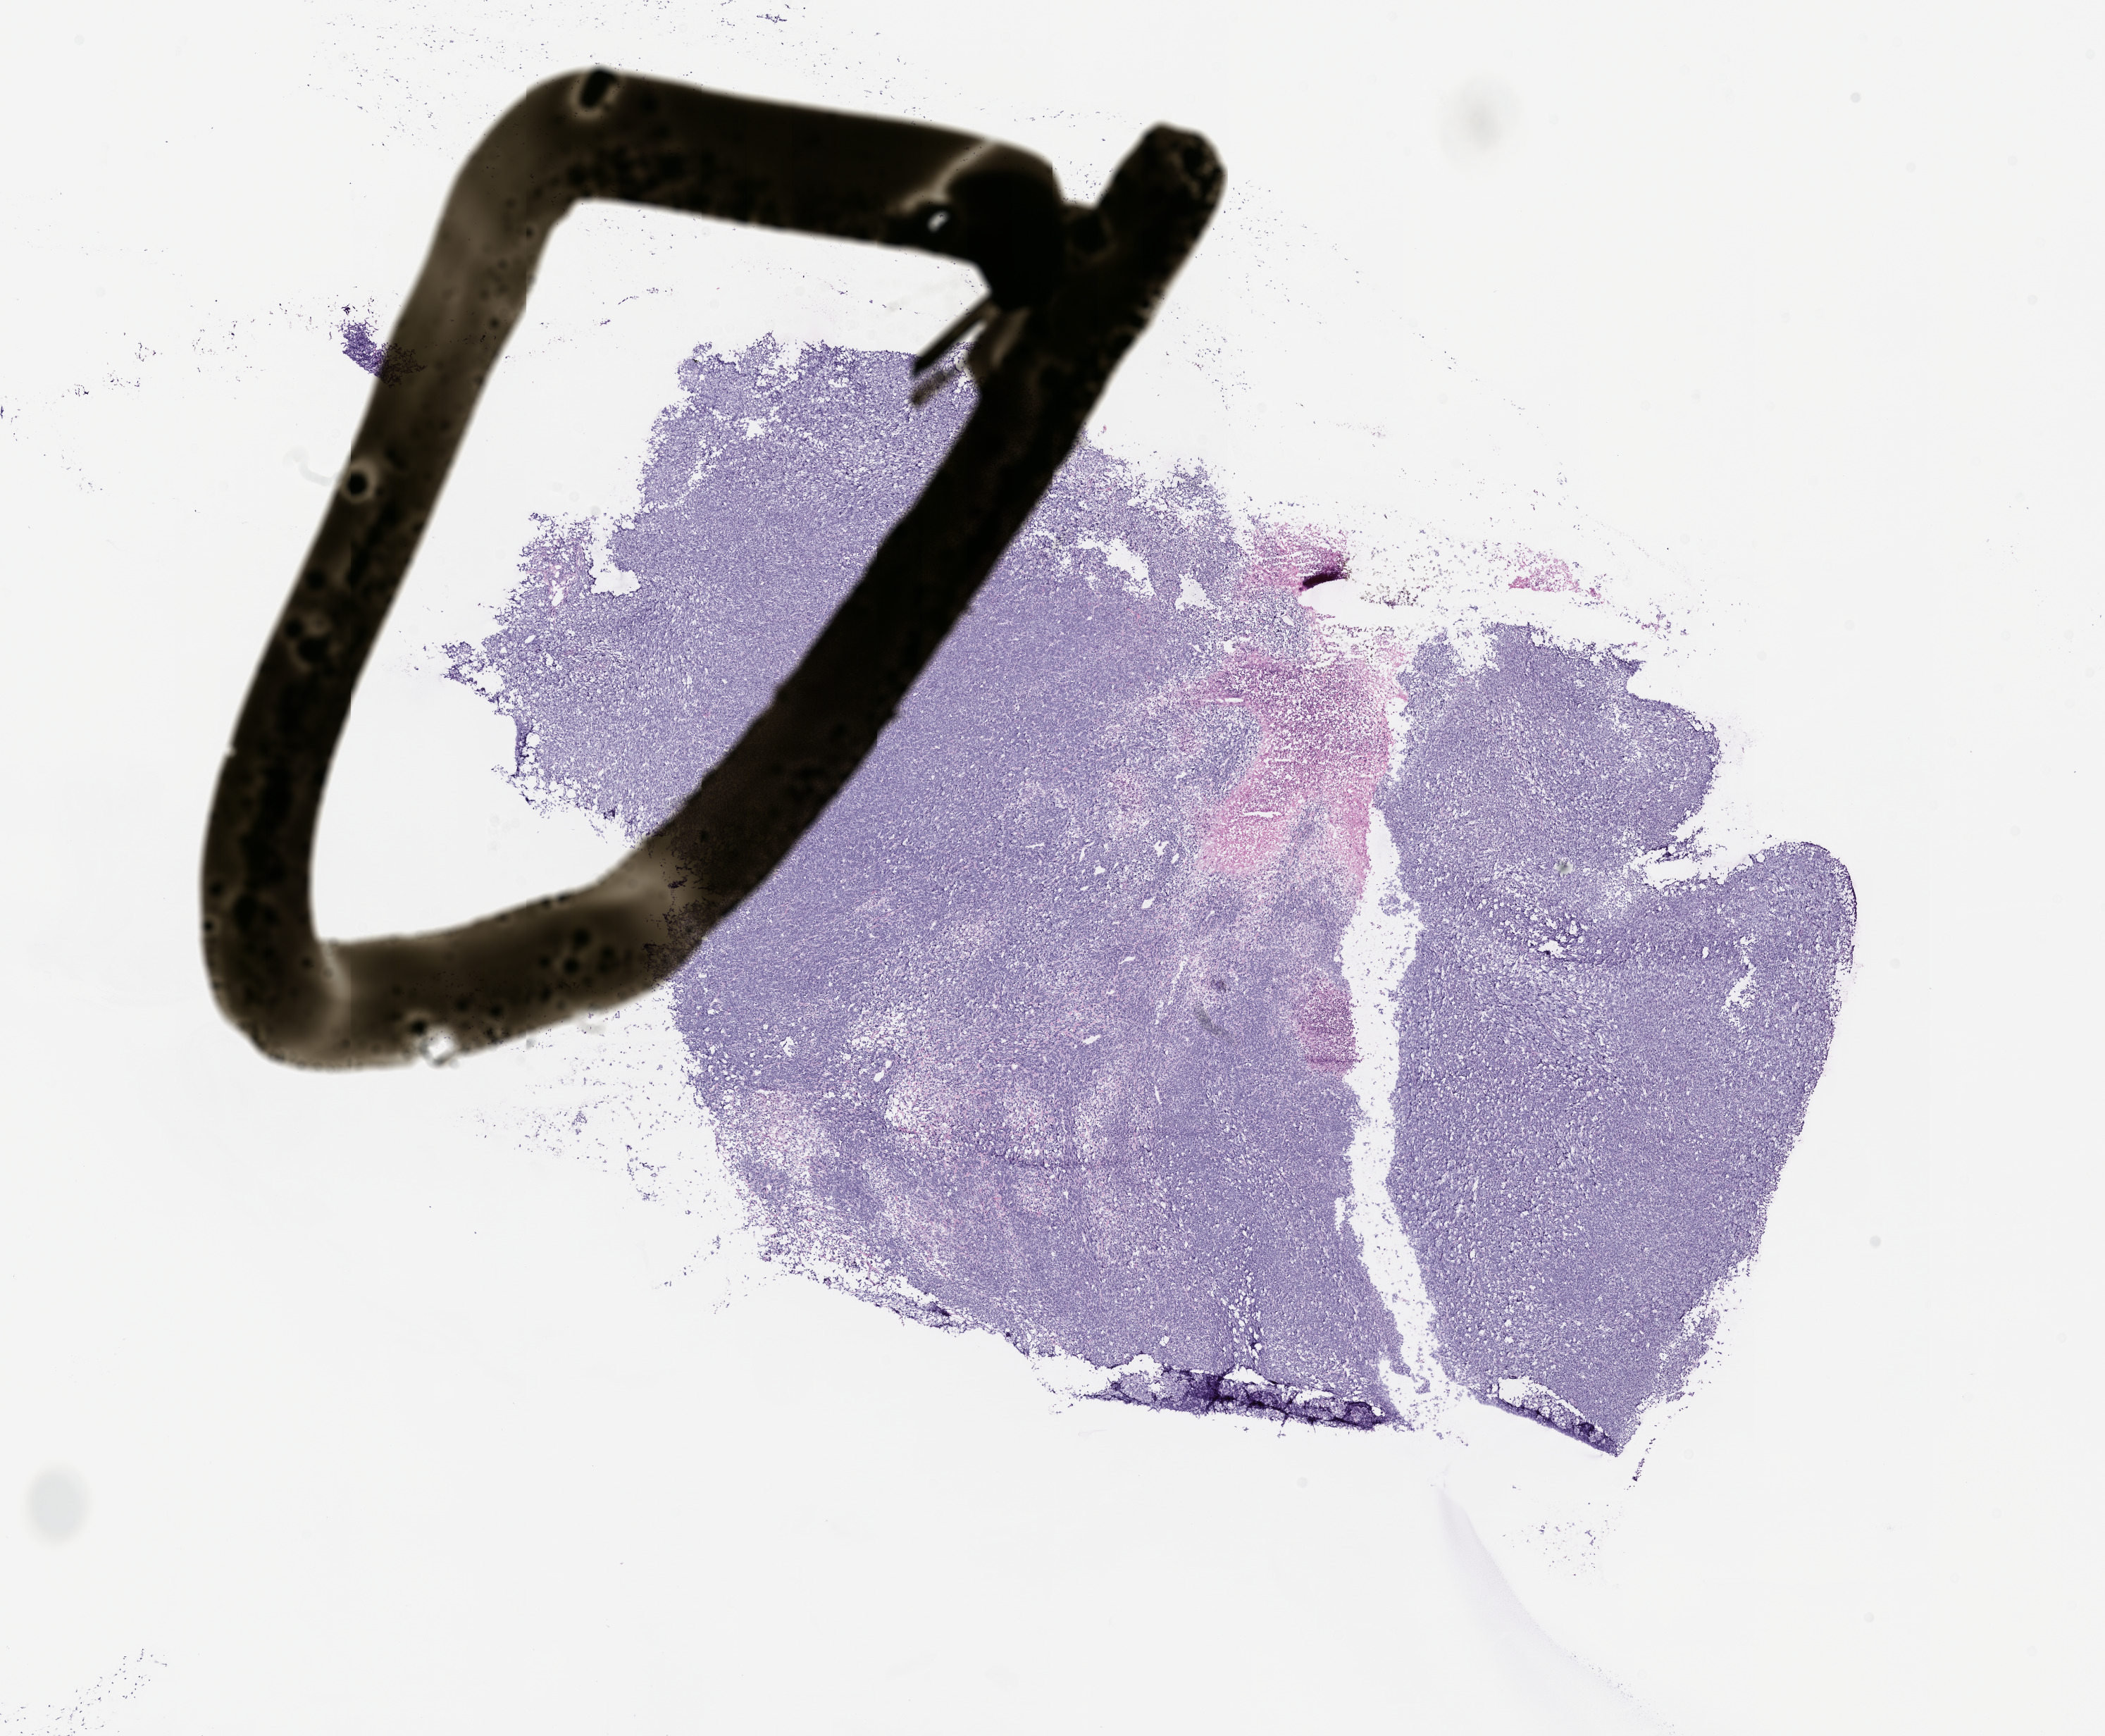
Whole-slide image, hematoxylin and eosin (H&E): patient-derived xenograft (human tumor grown in a mouse), passage 2, whole scanned area (about 12.0 x 9.9 mm) shown as a low-resolution overview. Formalin-fixed, paraffin-embedded (FFPE) tissue. Originating tumor site category: musculoskeletal.
Originating patient diagnosis: Synovial Sarcoma.